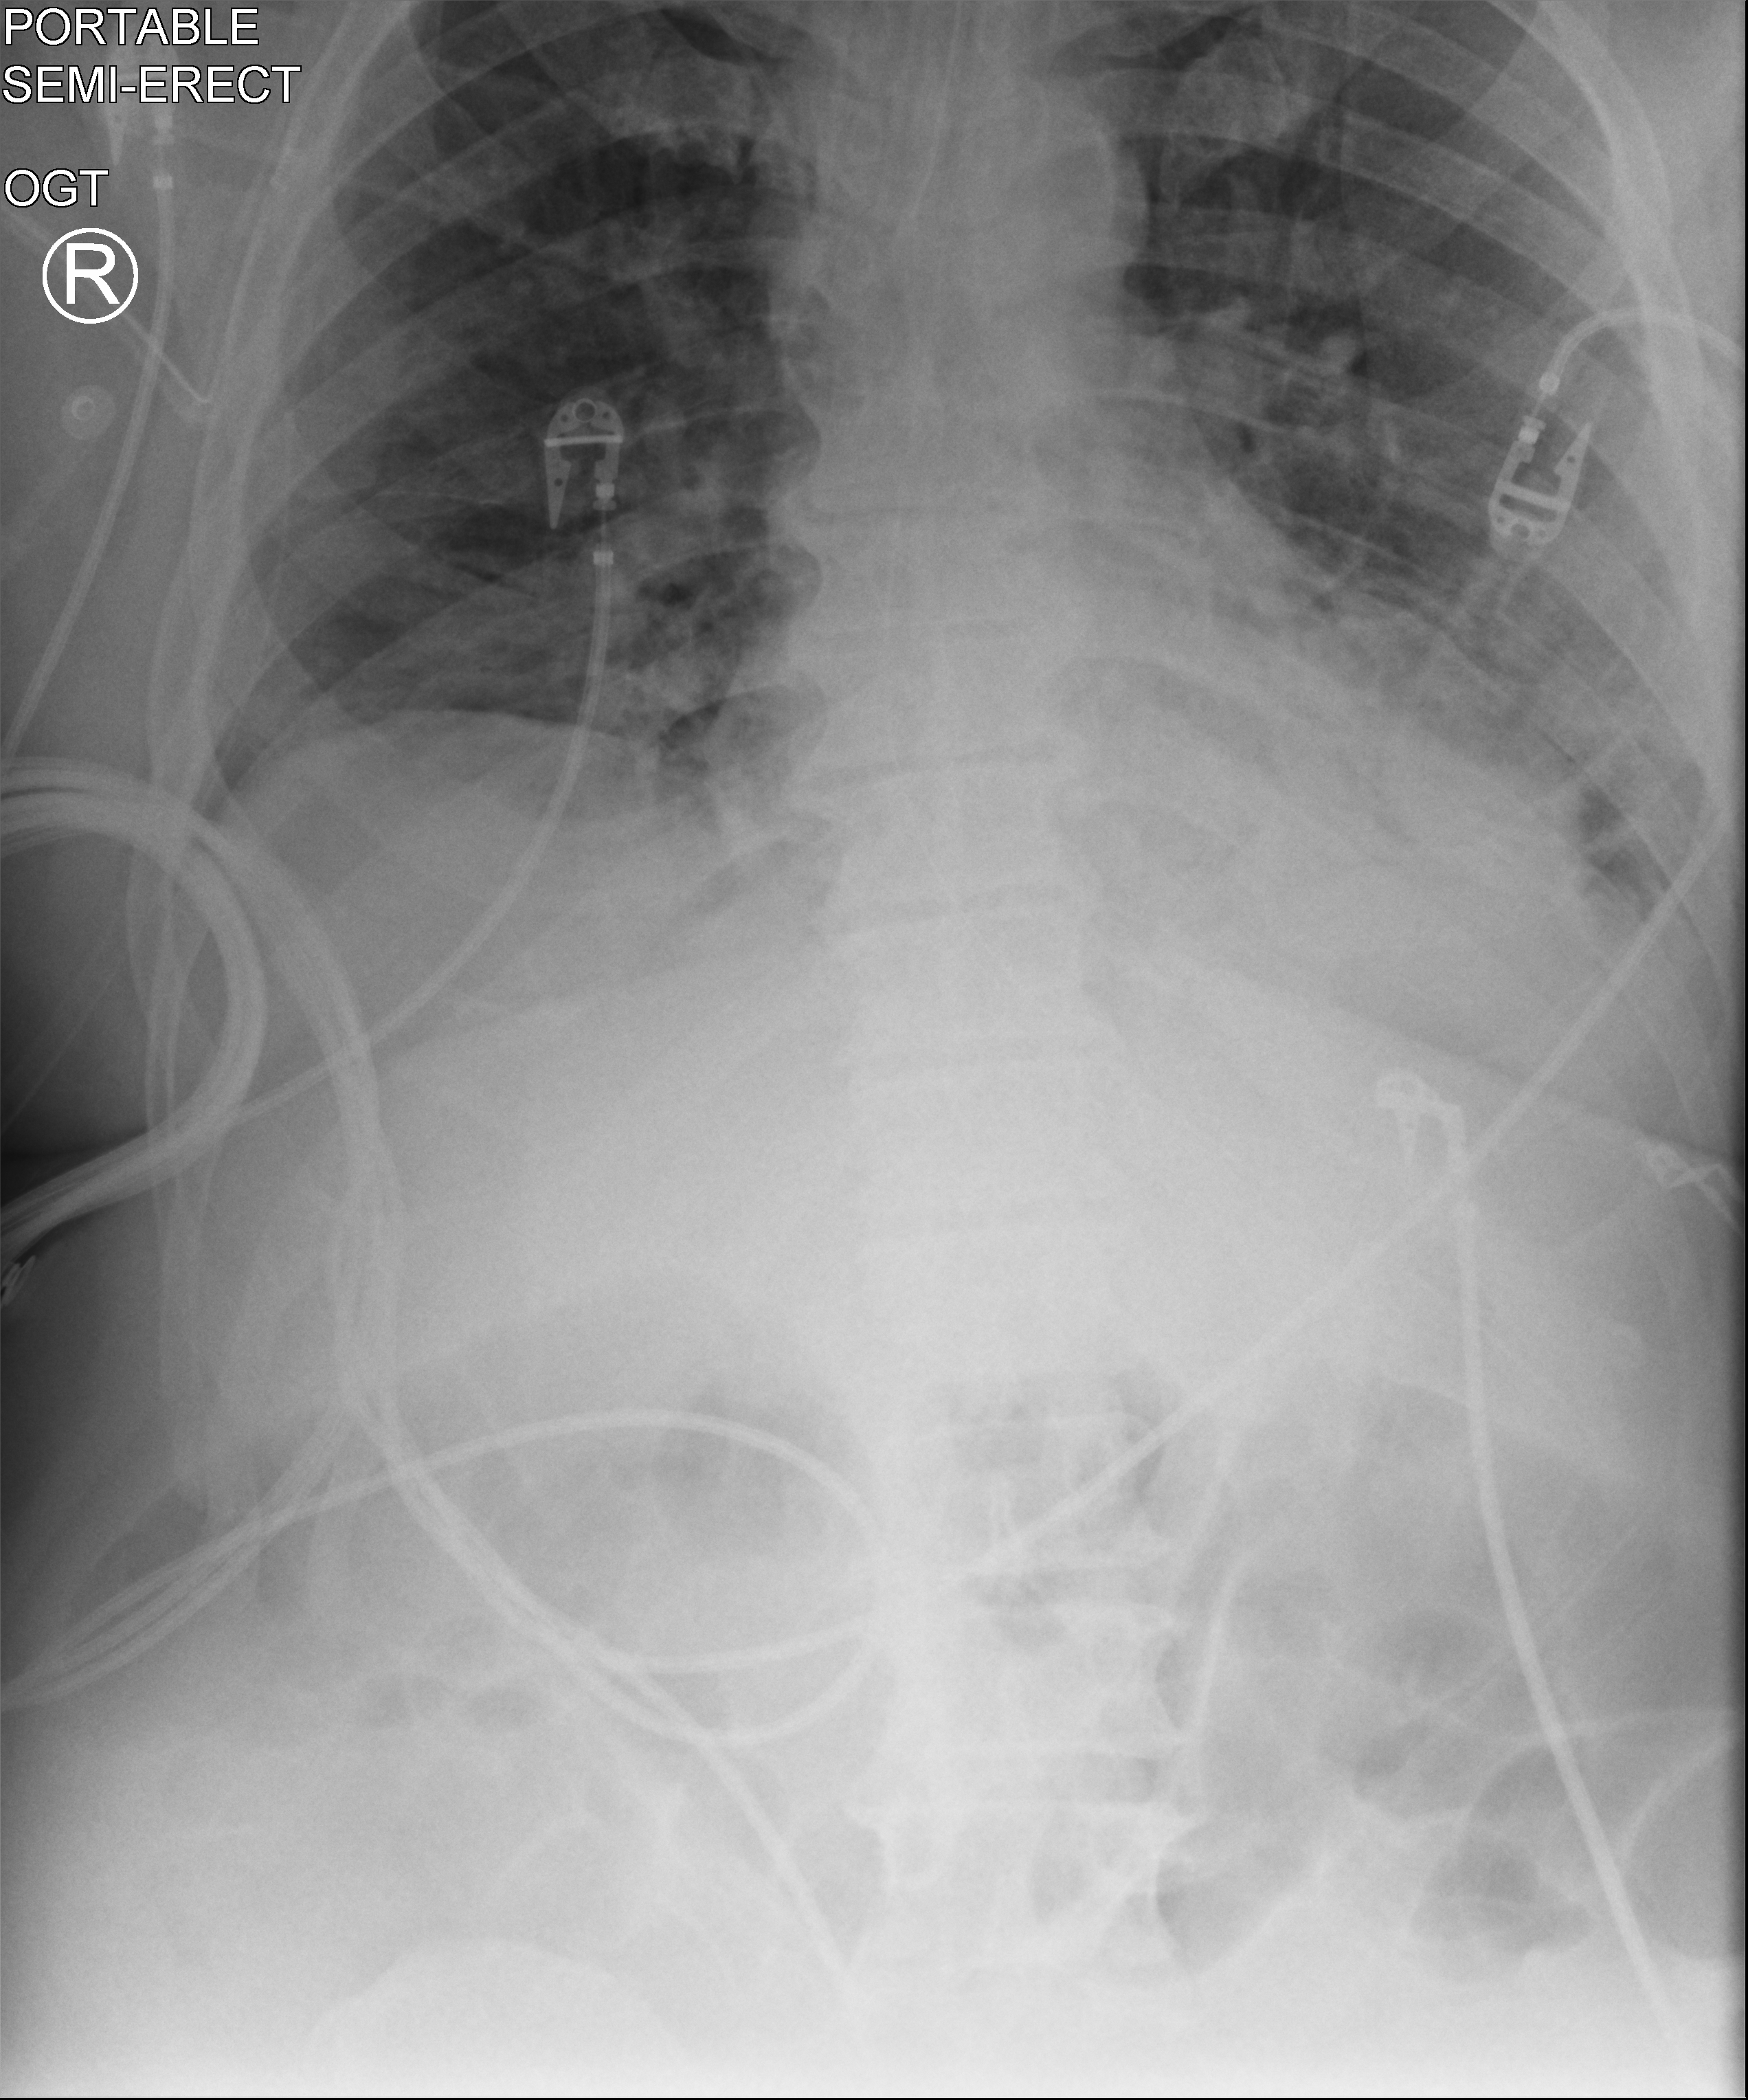
Portable chest radiograph, anteroposterior (AP) projection. Male patient hospitalised with COVID-19, age 18–59 years.
From the hospital-stay record, not from the radiograph (when in the stay this image was taken is not recorded): admitted to intensive care during this hospital stay: yes; mechanically ventilated during this hospital stay: yes.